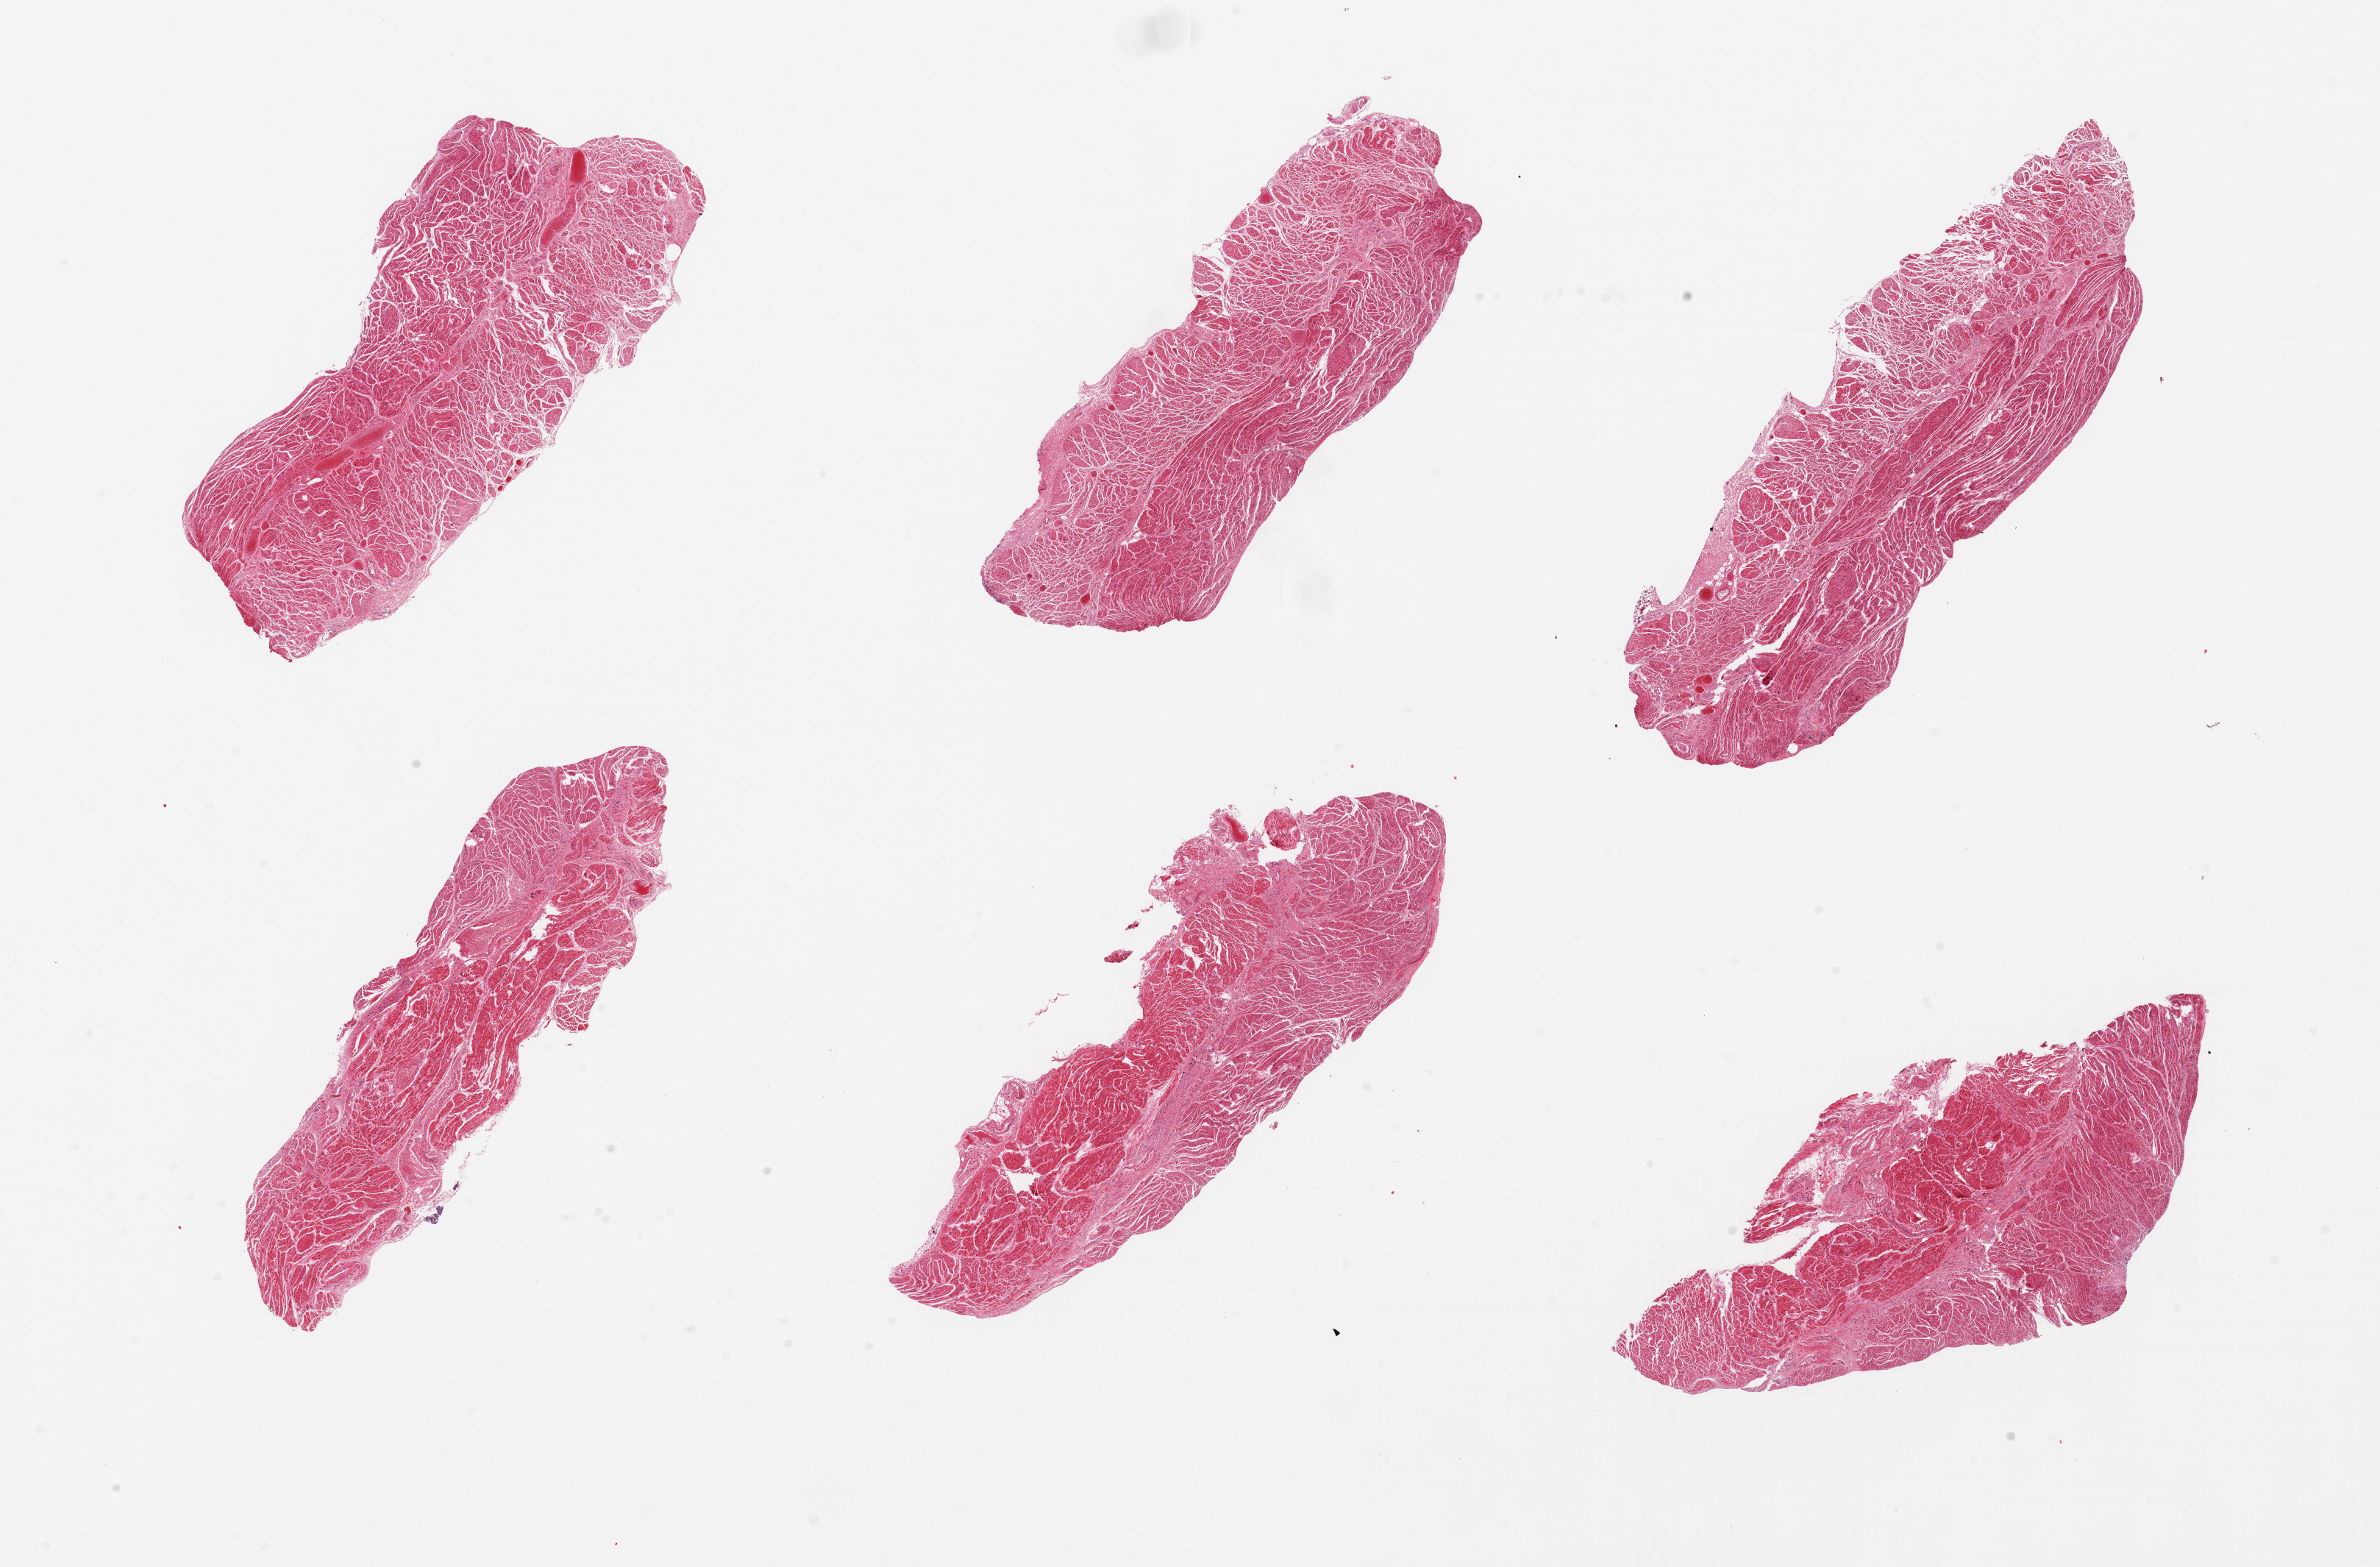
Whole-slide image, H&E stain, low-resolution overview of the scanned area, about 25.6 x 16.8 mm, PAXgene-fixed paraffin-embedded (PFPE) section, target tissue: gastroesophageal junction, tissue donor sample. Donor sex: female.
- review note (as recorded): 6 pieces; well trimmed muscularis